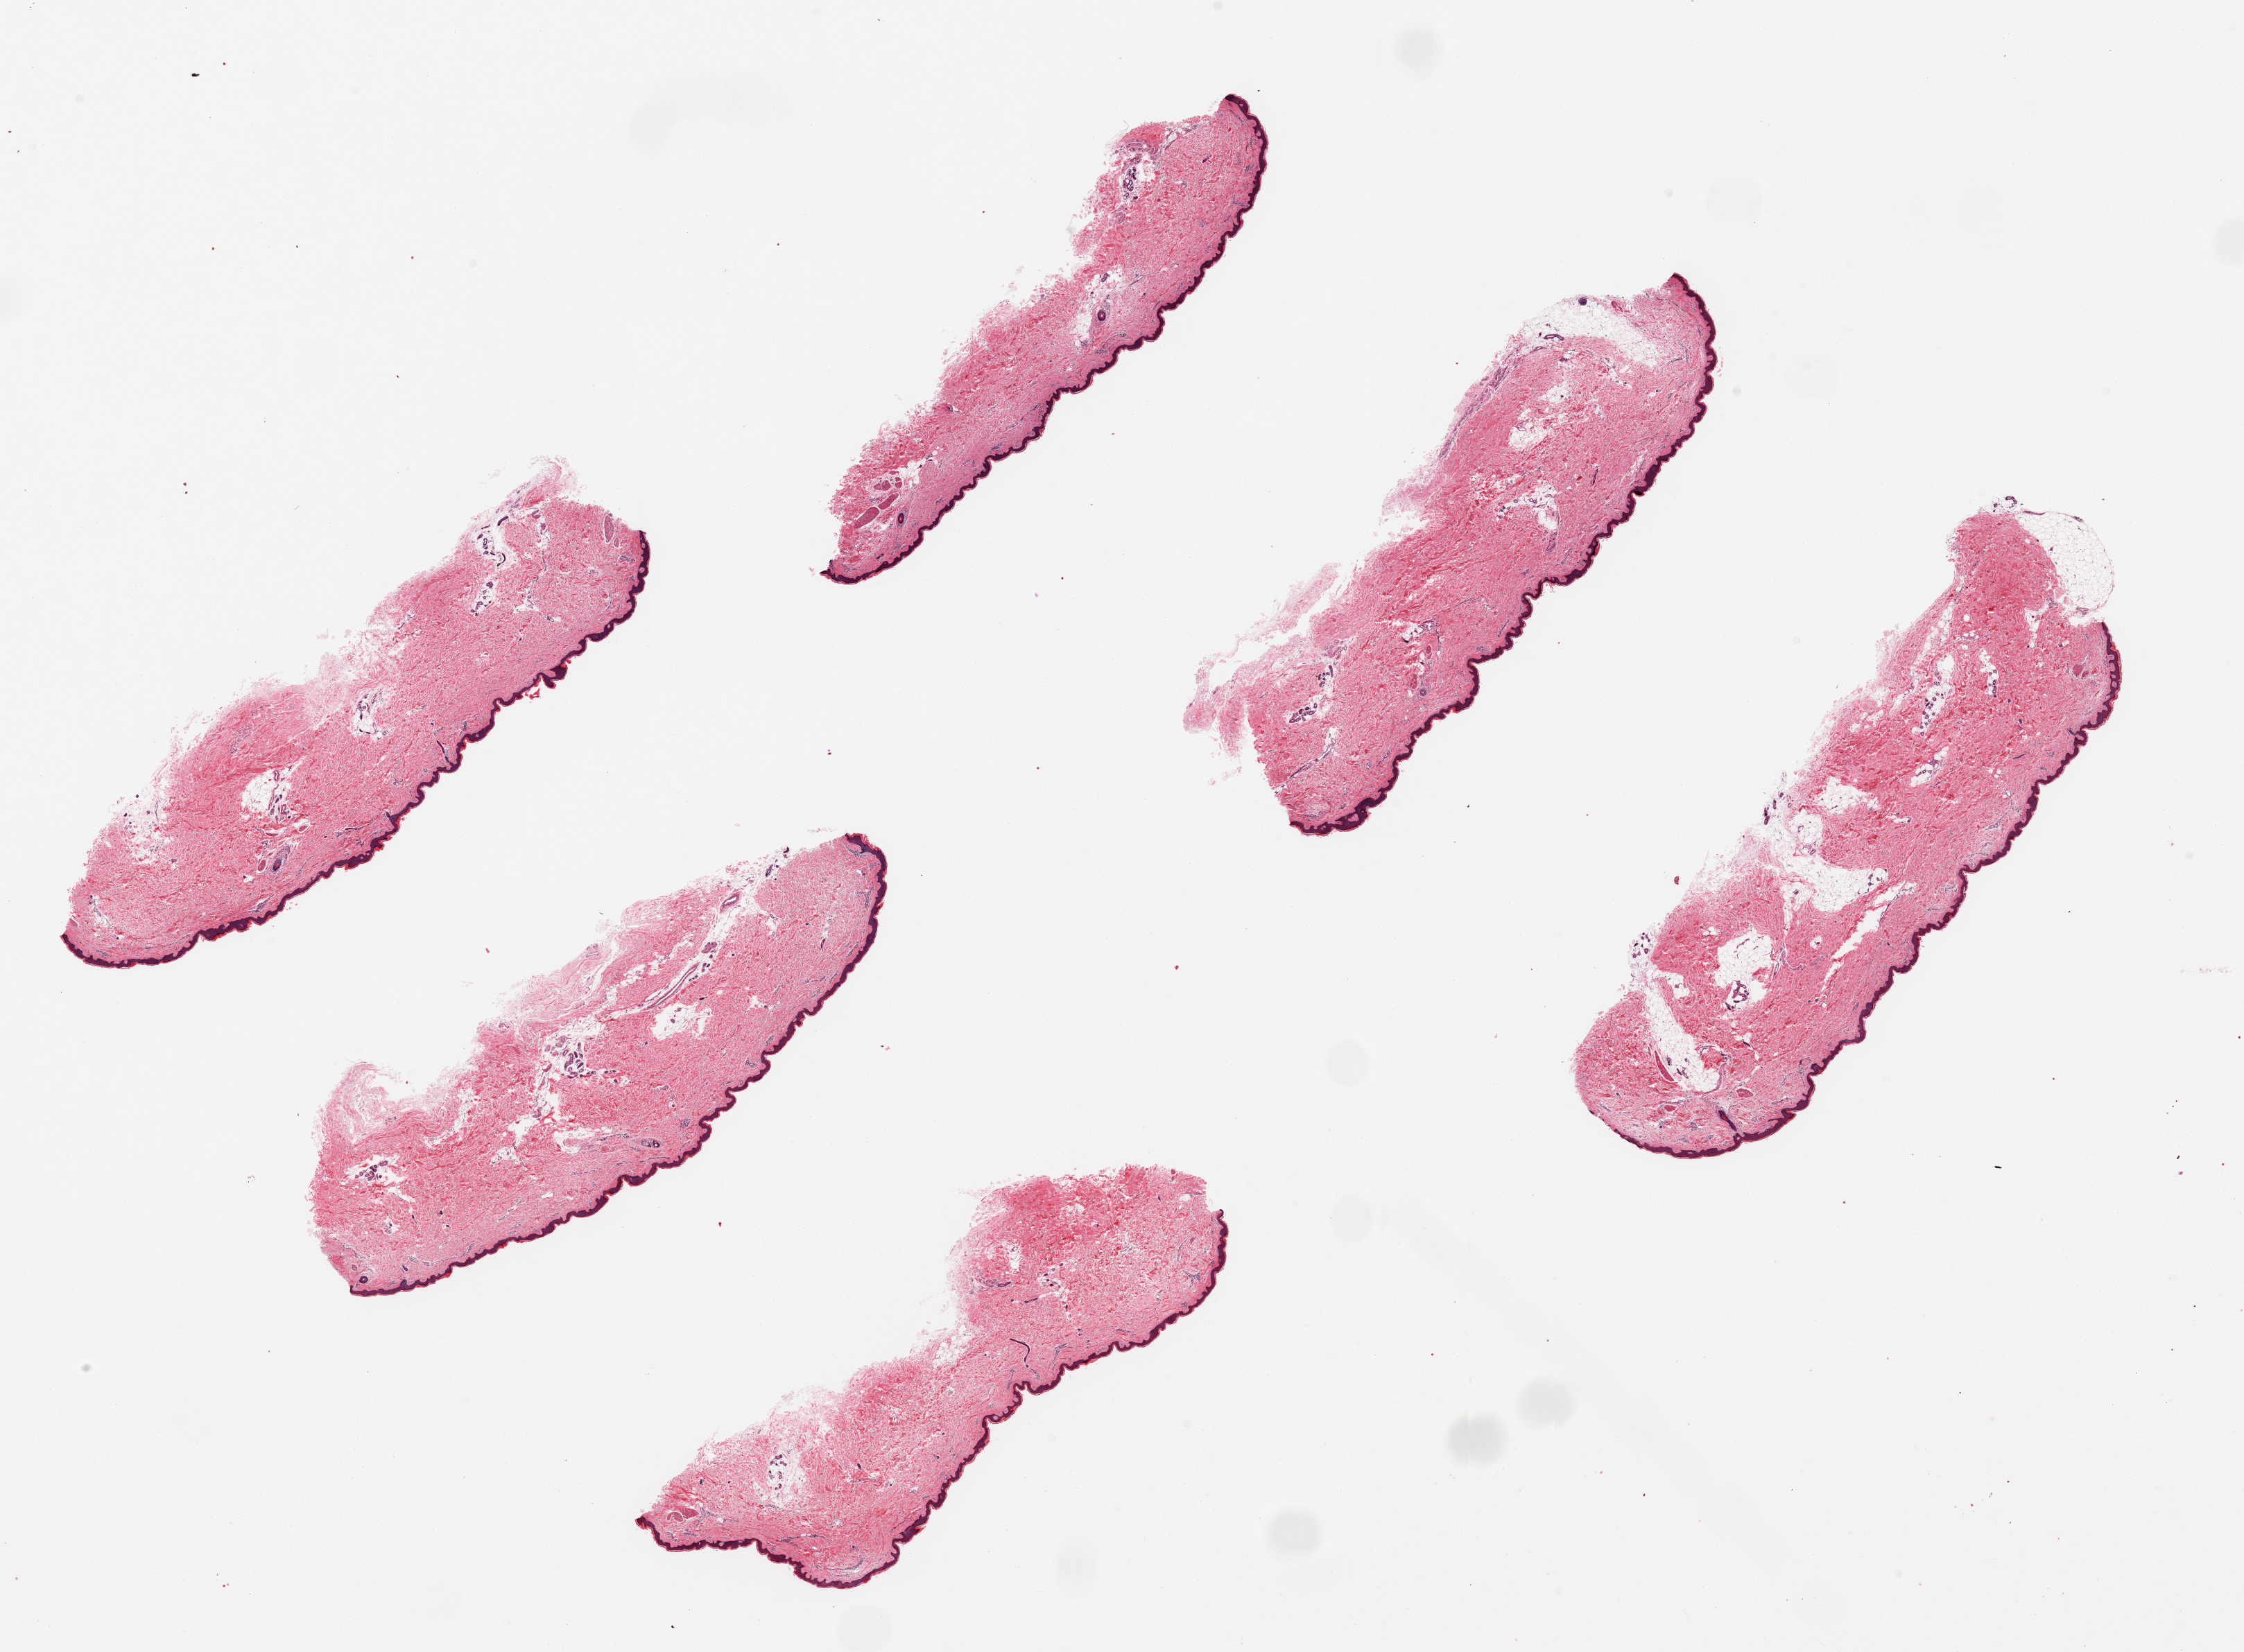
H&E whole-slide image — low-resolution overview of the scanned area, about 25.6 x 18.8 mm (from a 20x scan). PAXgene-fixed, paraffin-embedded tissue. Target tissue: skin of lower leg. Tissue donor sample. Donor sex: female.
Pathologist's review note for this sample: 6 pieces up to 8x2.5 mm.